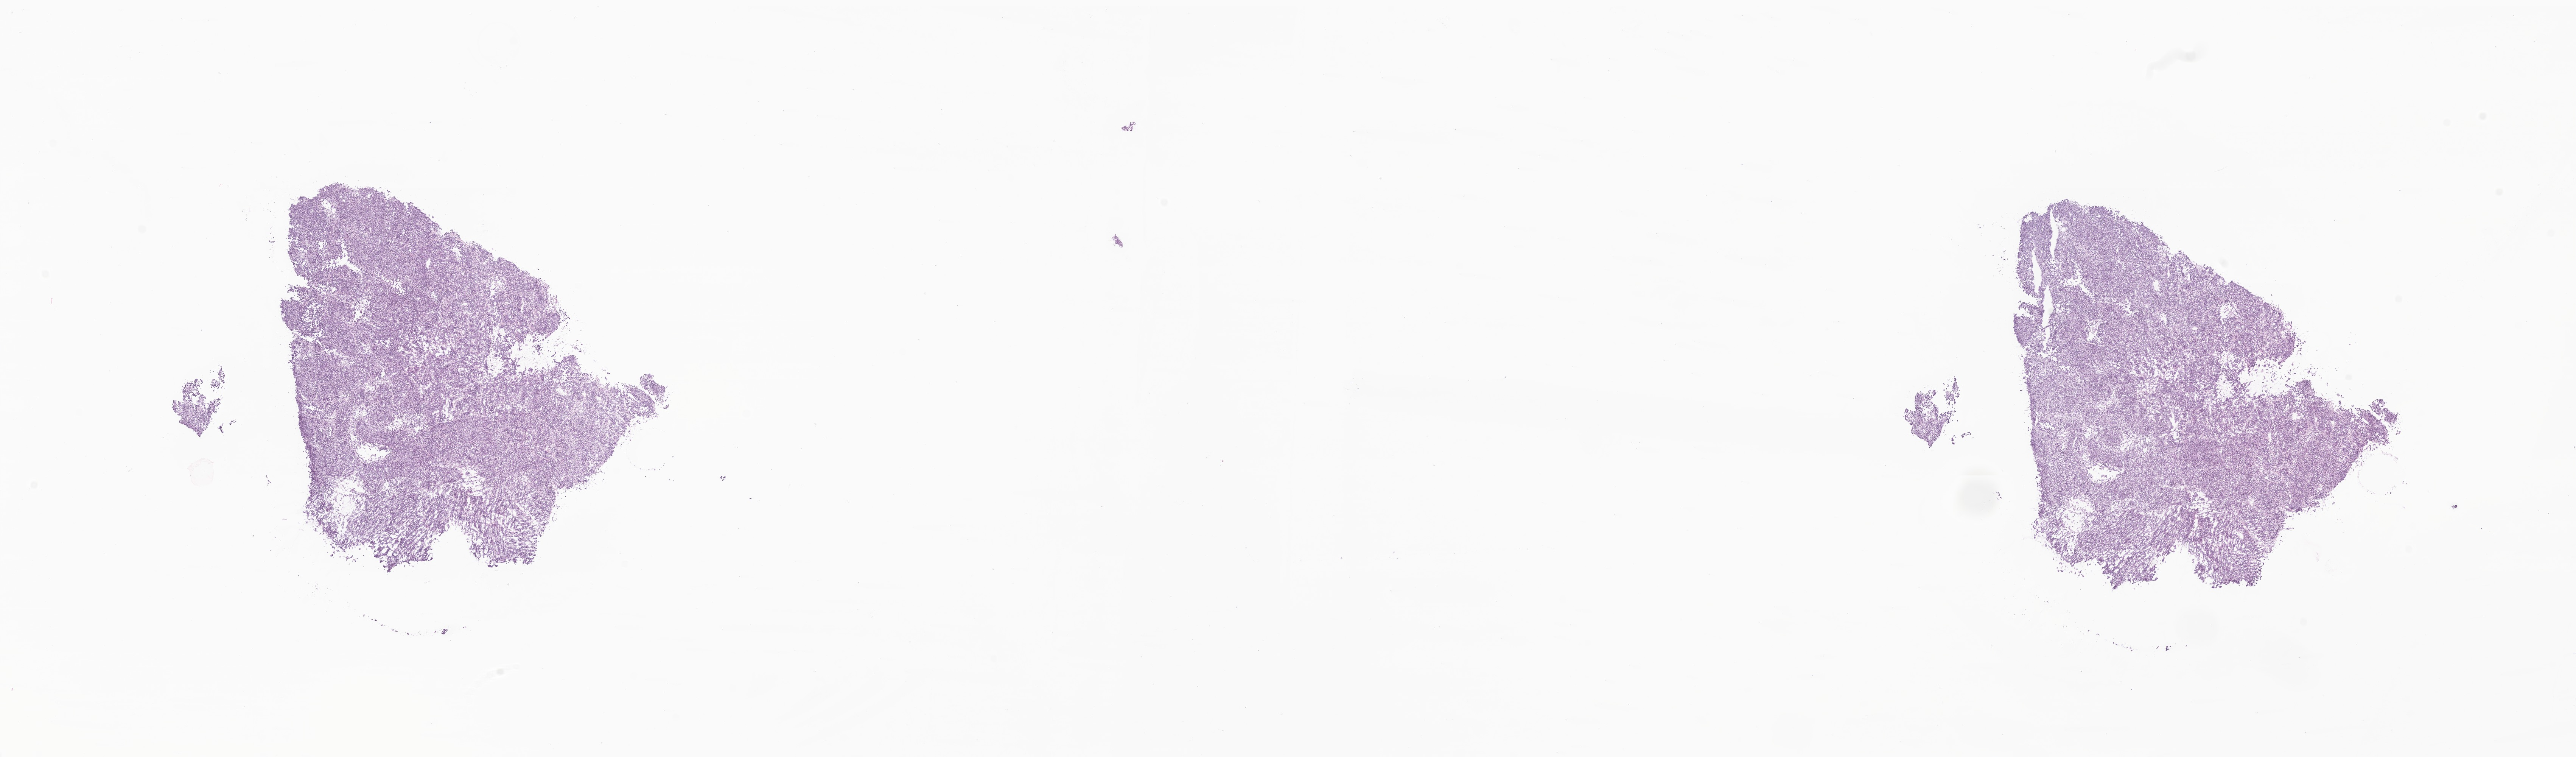
Hematoxylin and eosin (H&E) whole-slide image of tumor tissue from the breast, whole scanned area (about 28.7 x 8.4 mm) shown as a low-resolution overview, frozen section. Patient female; age 184 months (15 years 4 months).
Diagnosis (ICD-O-3 morphology term): Angiomyosarcoma.